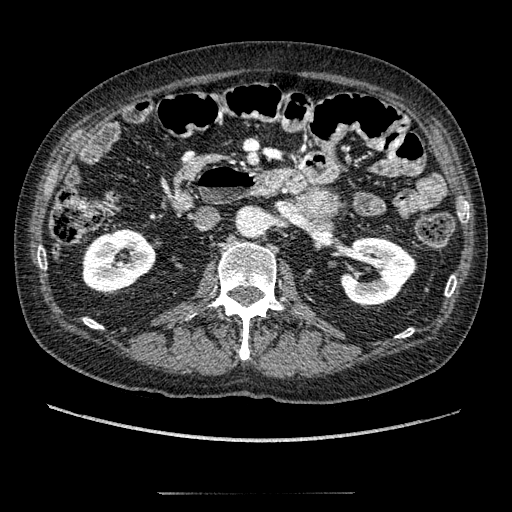
Contrast-enhanced abdominal CT, one axial slice; reconstruction kernel STANDARD; intravenous contrast given; soft-tissue window (W 400 / L 40 HU); 1.25 mm slice thickness; 512 × 512 image matrix. Male patient, age 69 years. From the clinical record (not read from this slice): diagnosis: adrenocortical carcinoma; tumour side: left adrenal.
Structures marked on this image (semi-automatically segmented with operator editing):
- mass: bounding box [x1, y1, x2, y2] px = [299, 190, 338, 223]